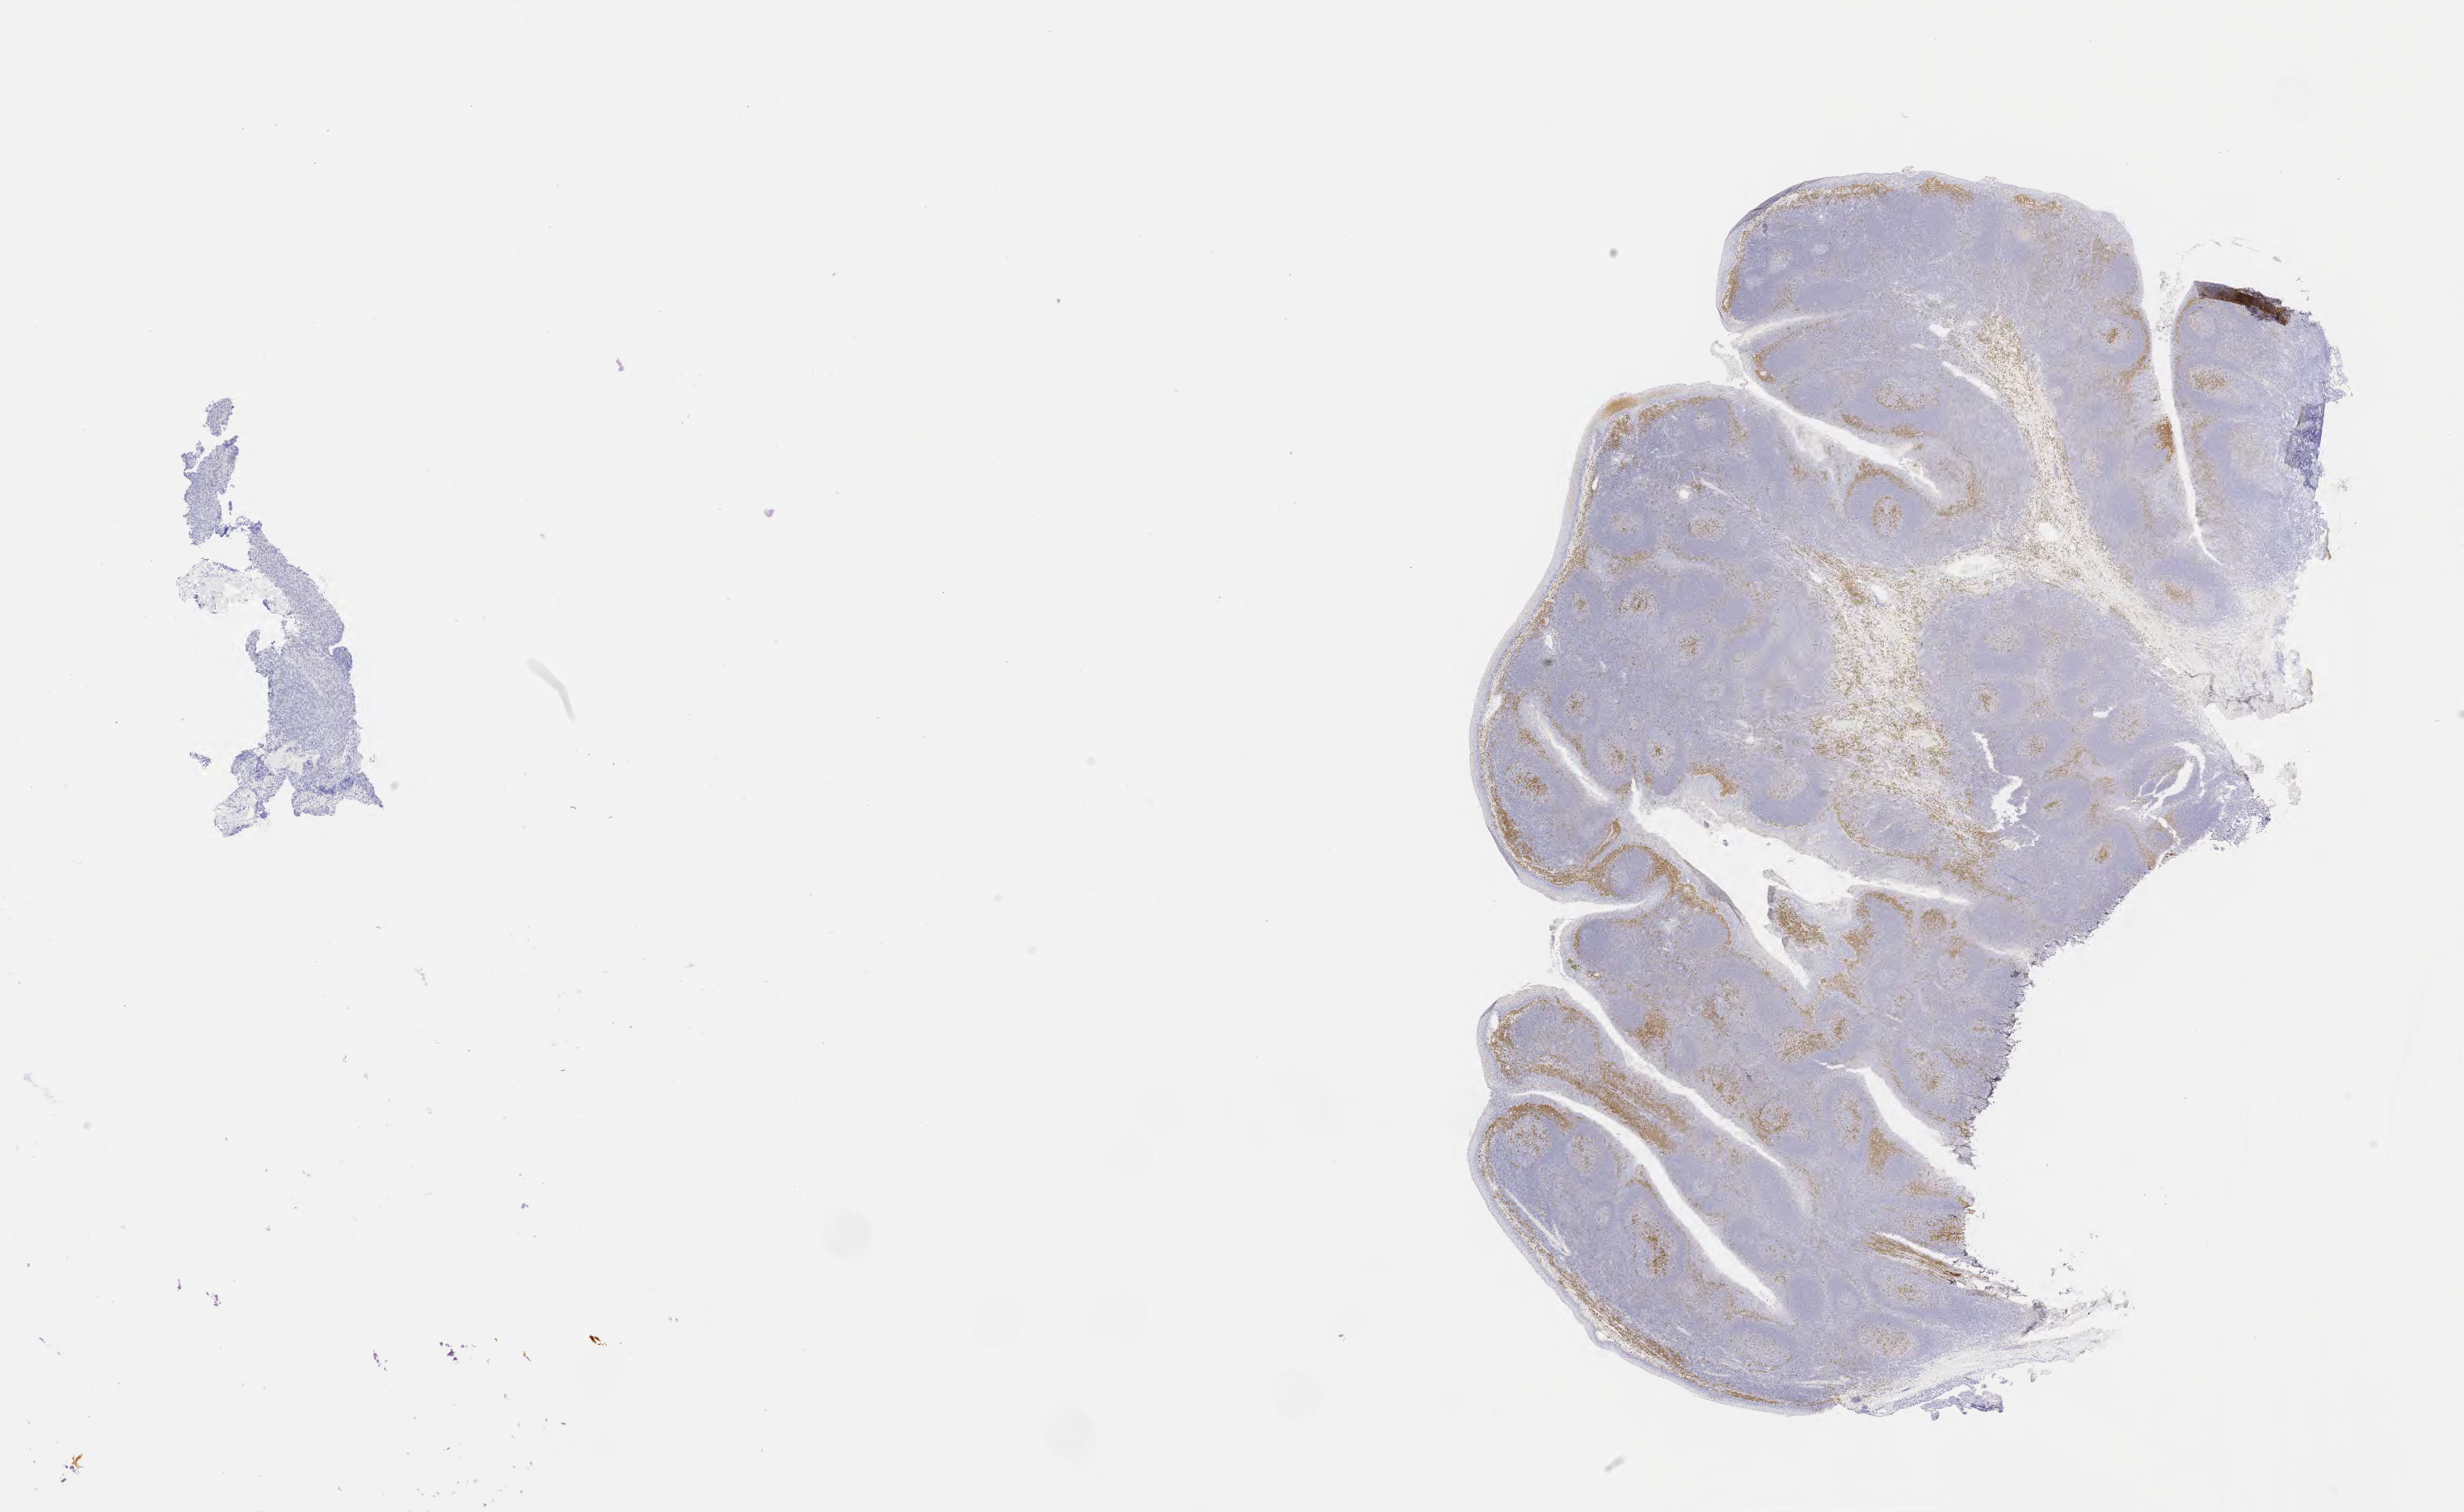
Immunohistochemistry (IHC) whole-slide image stained for IRF4/MUM1 — whole scanned area (about 24.6 x 15.1 mm) shown as a low-resolution overview. Tumor tissue. Female patient, aged 27.
Histologic diagnosis: Diffuse large B-cell lymphoma, NOS.